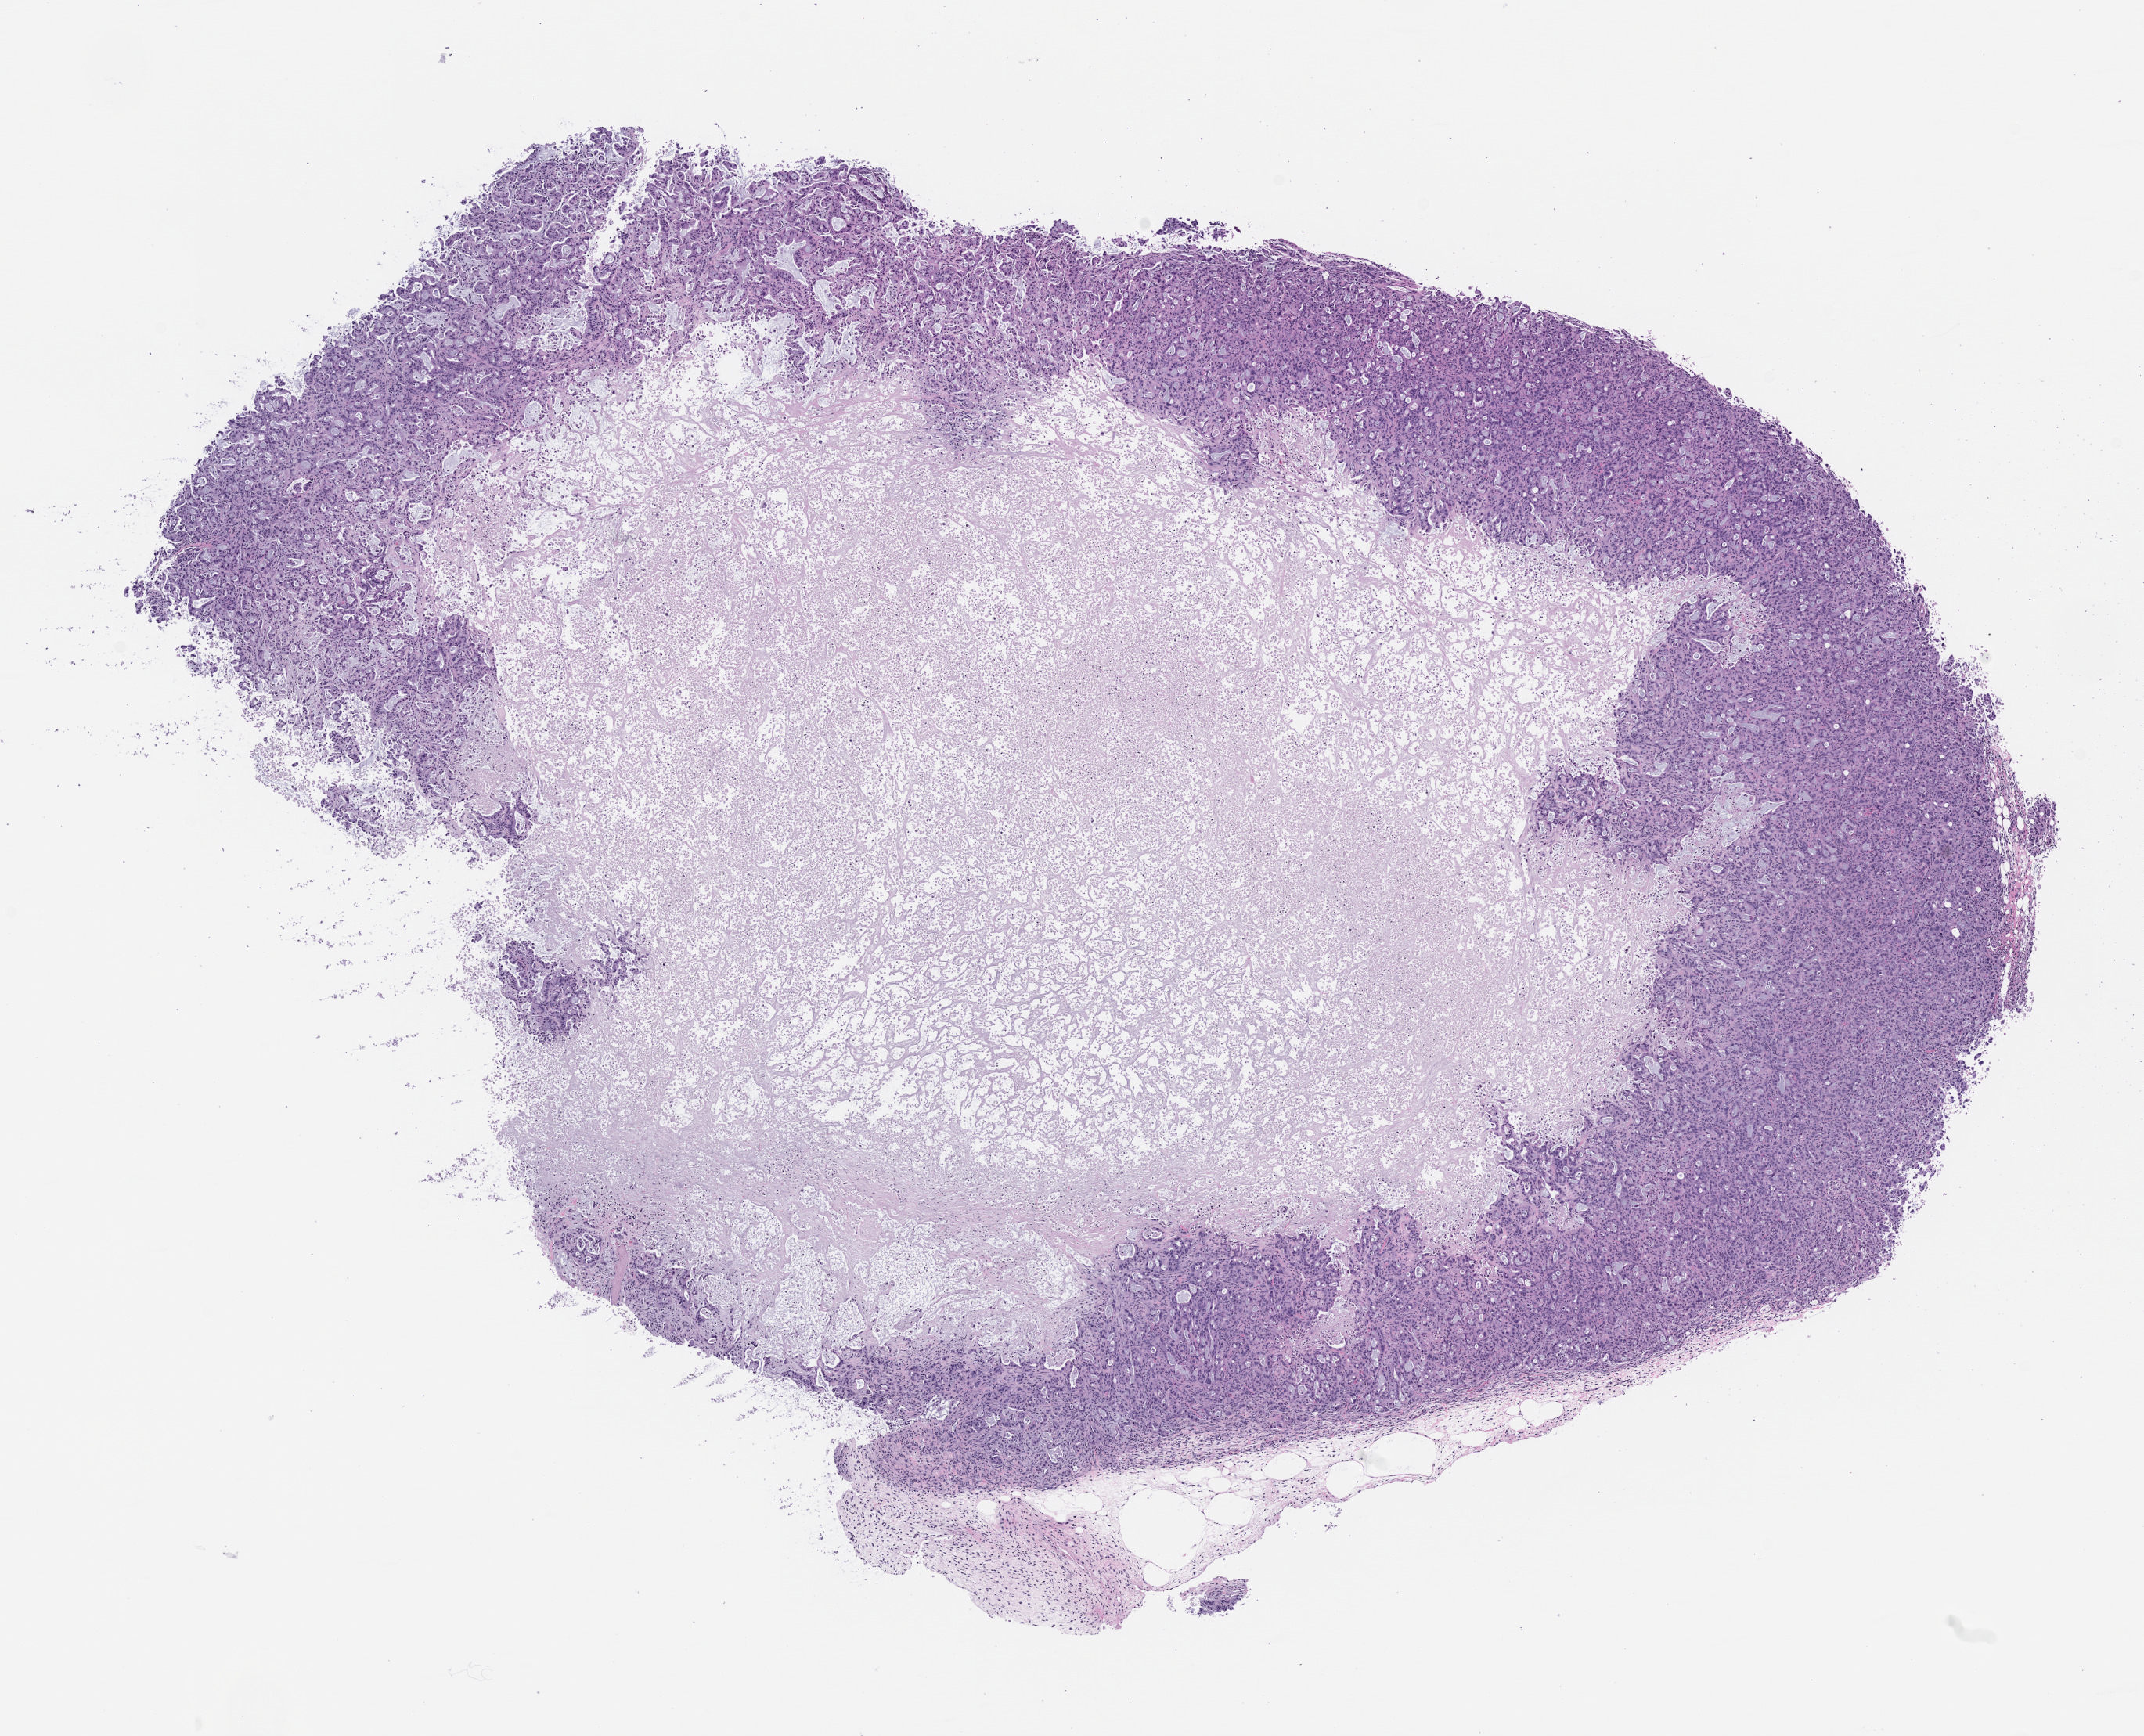
Whole-slide image, H&E: patient-derived xenograft (human tumor grown in a mouse), passage 2 — a low-resolution overview of the entire scanned area, about 11.0 x 8.9 mm. Formalin-fixed, paraffin-embedded (FFPE) tissue. Originating tumor site category: pancreas.
Originating patient diagnosis: Pancreatic Adenocarcinoma.